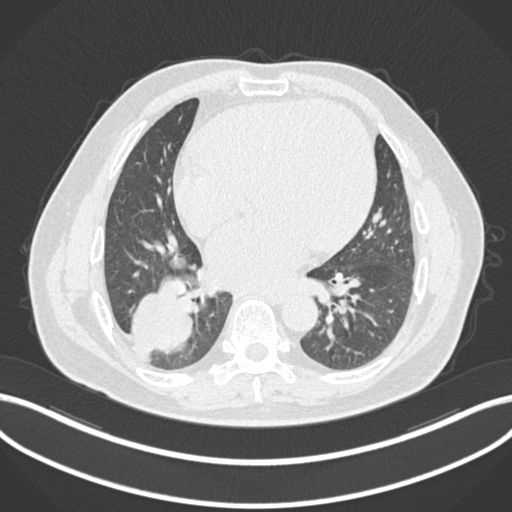
Chest CT, one axial slice; reconstruction kernel B30f; lung window (W 1500 / L -600 HU); 1 mm slice thickness; 512 × 512 image matrix. Patient: male, 59 years.
Structures marked on this image (rectangle marked by the reading radiologist):
- lung tumour (recorded histology: adenocarcinoma): bounding box <132,273,199,357> (left, top, right, bottom; pixels)